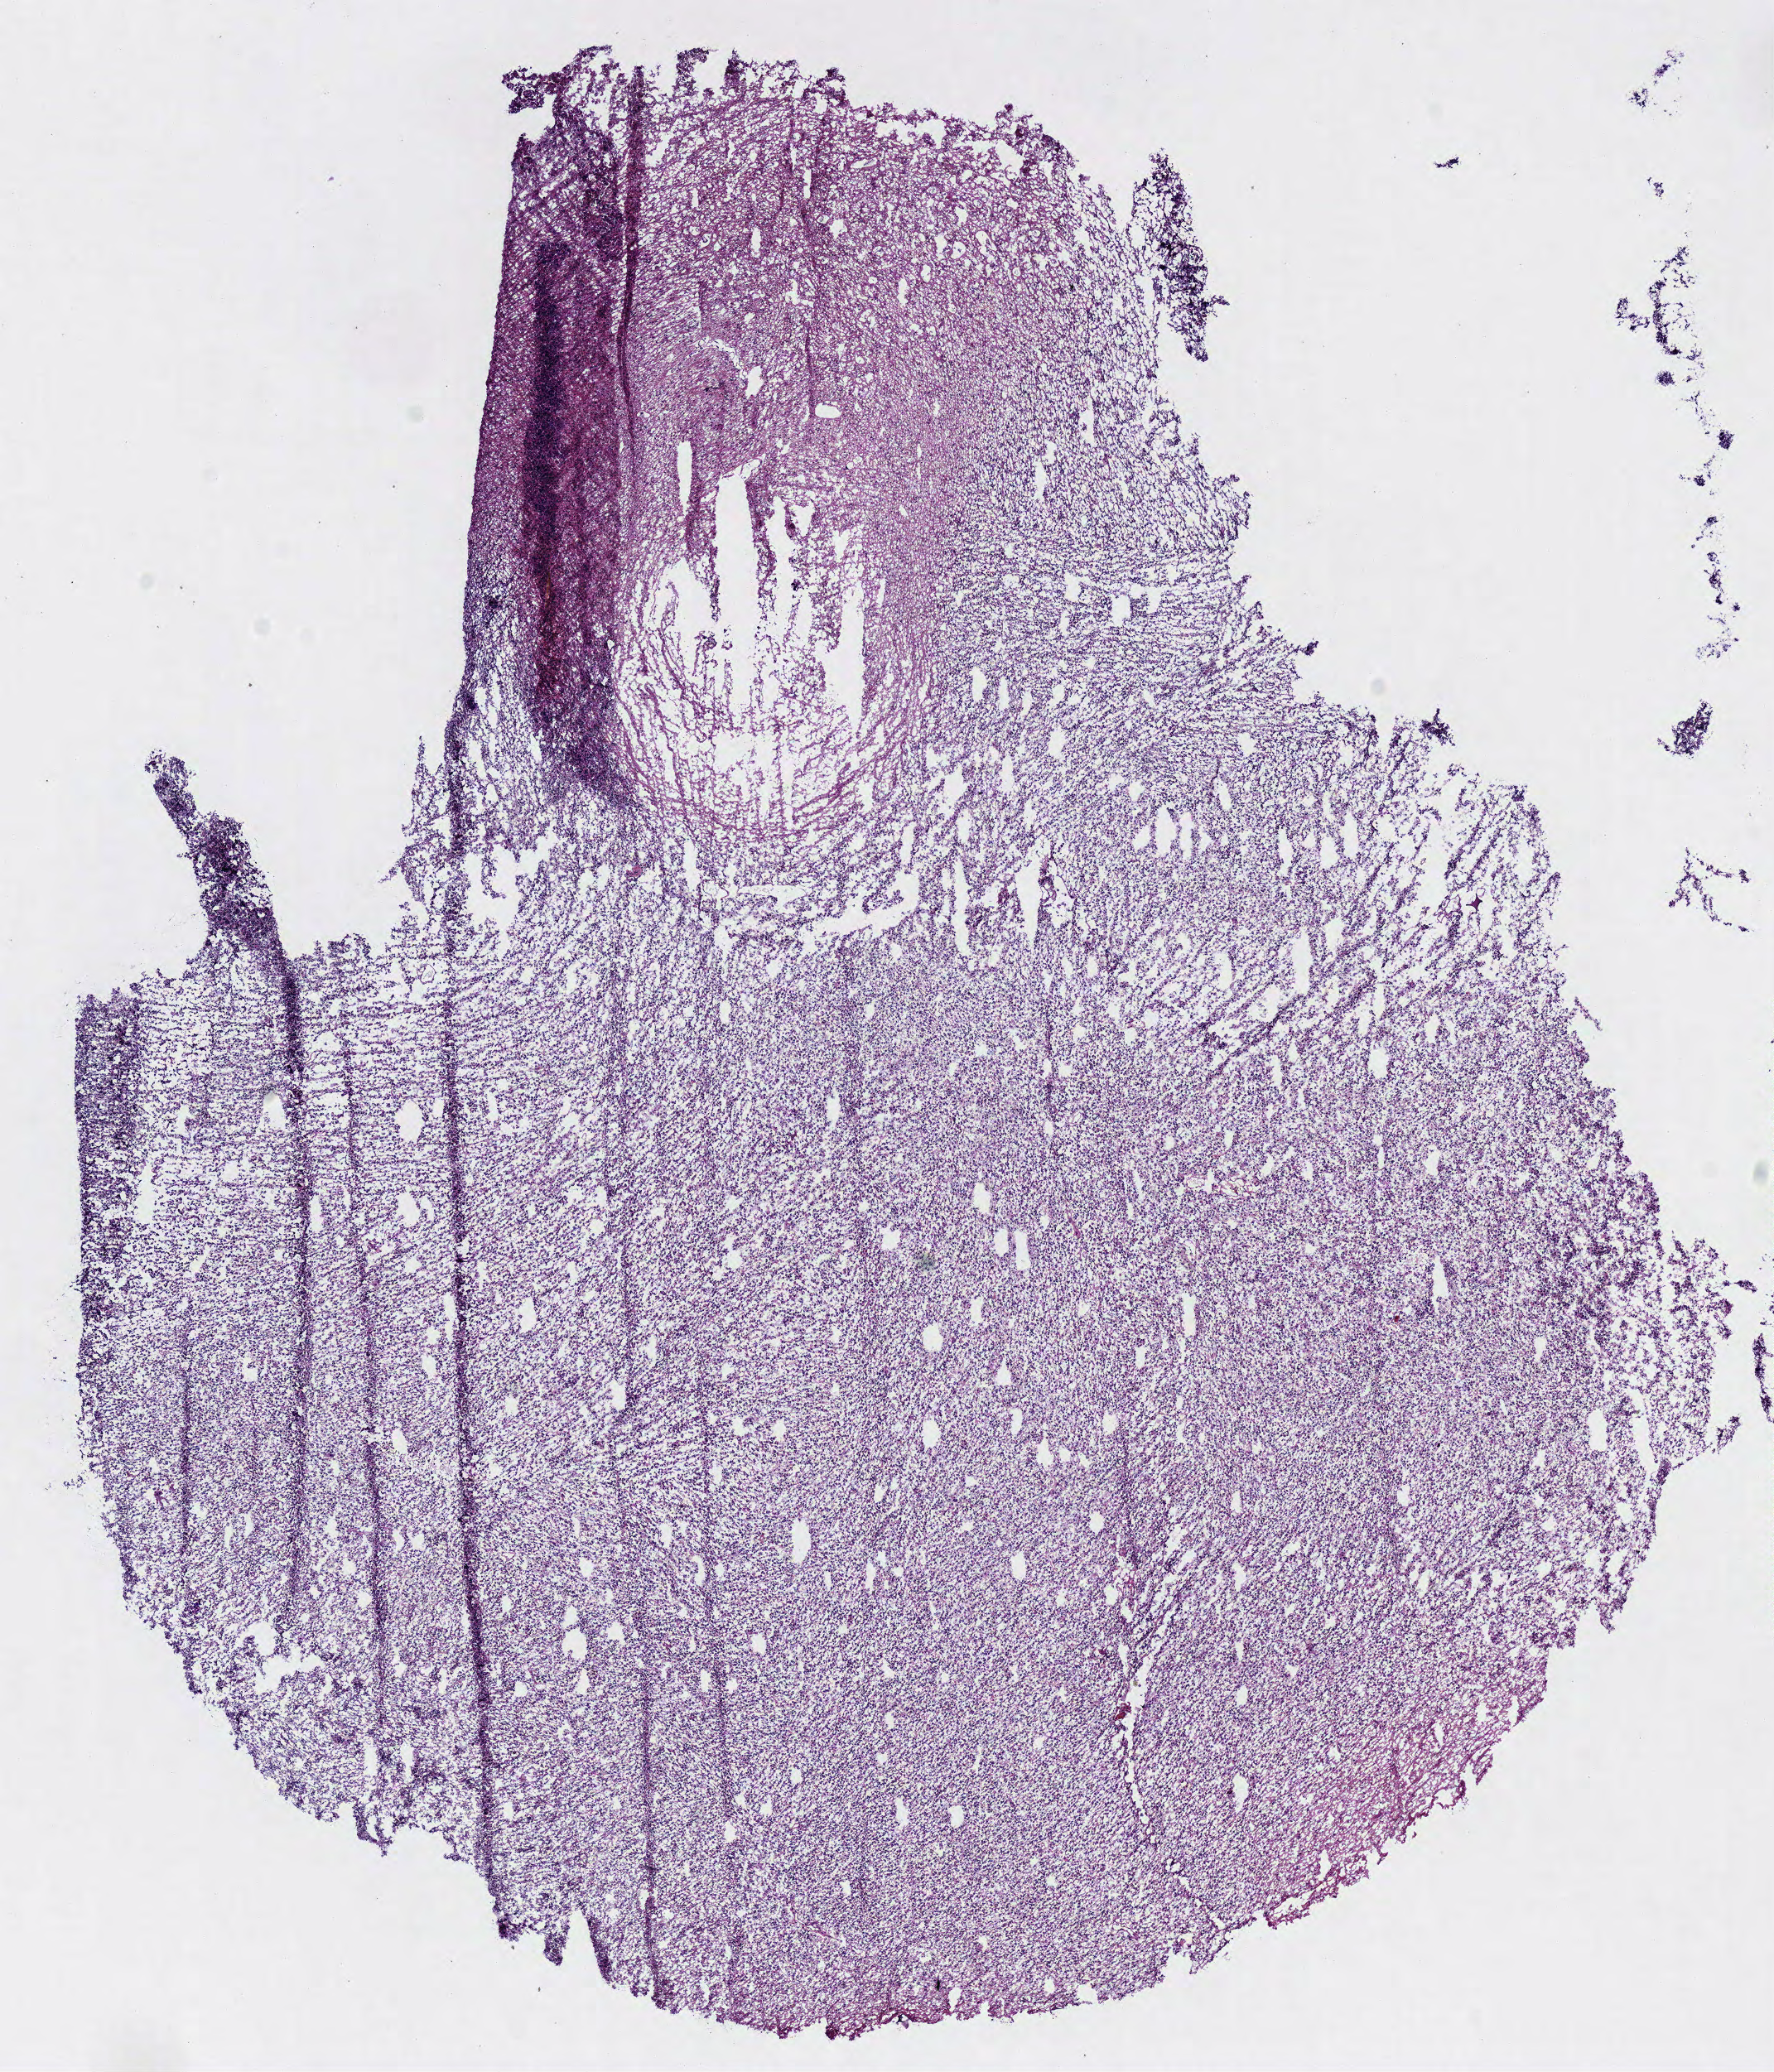
Digitized Hematoxylin and eosin (H&E) stained tissue section (whole slide) — low-resolution overview of the scanned area, about 8.4 x 9.9 mm (from a 40x scan); frozen section from the bottom of the tissue portion; brain, primary tumour sample. Female patient; age at initial diagnosis 62 years. Histologic grade: G2 (moderately differentiated). Composition of this section per pathologist review: tumour cells 100%, tumour nuclei 75%, normal cells 0%, stromal cells 0%, necrosis 0%.
* laterality: left
* diagnosis: Oligodendroglioma, NOS